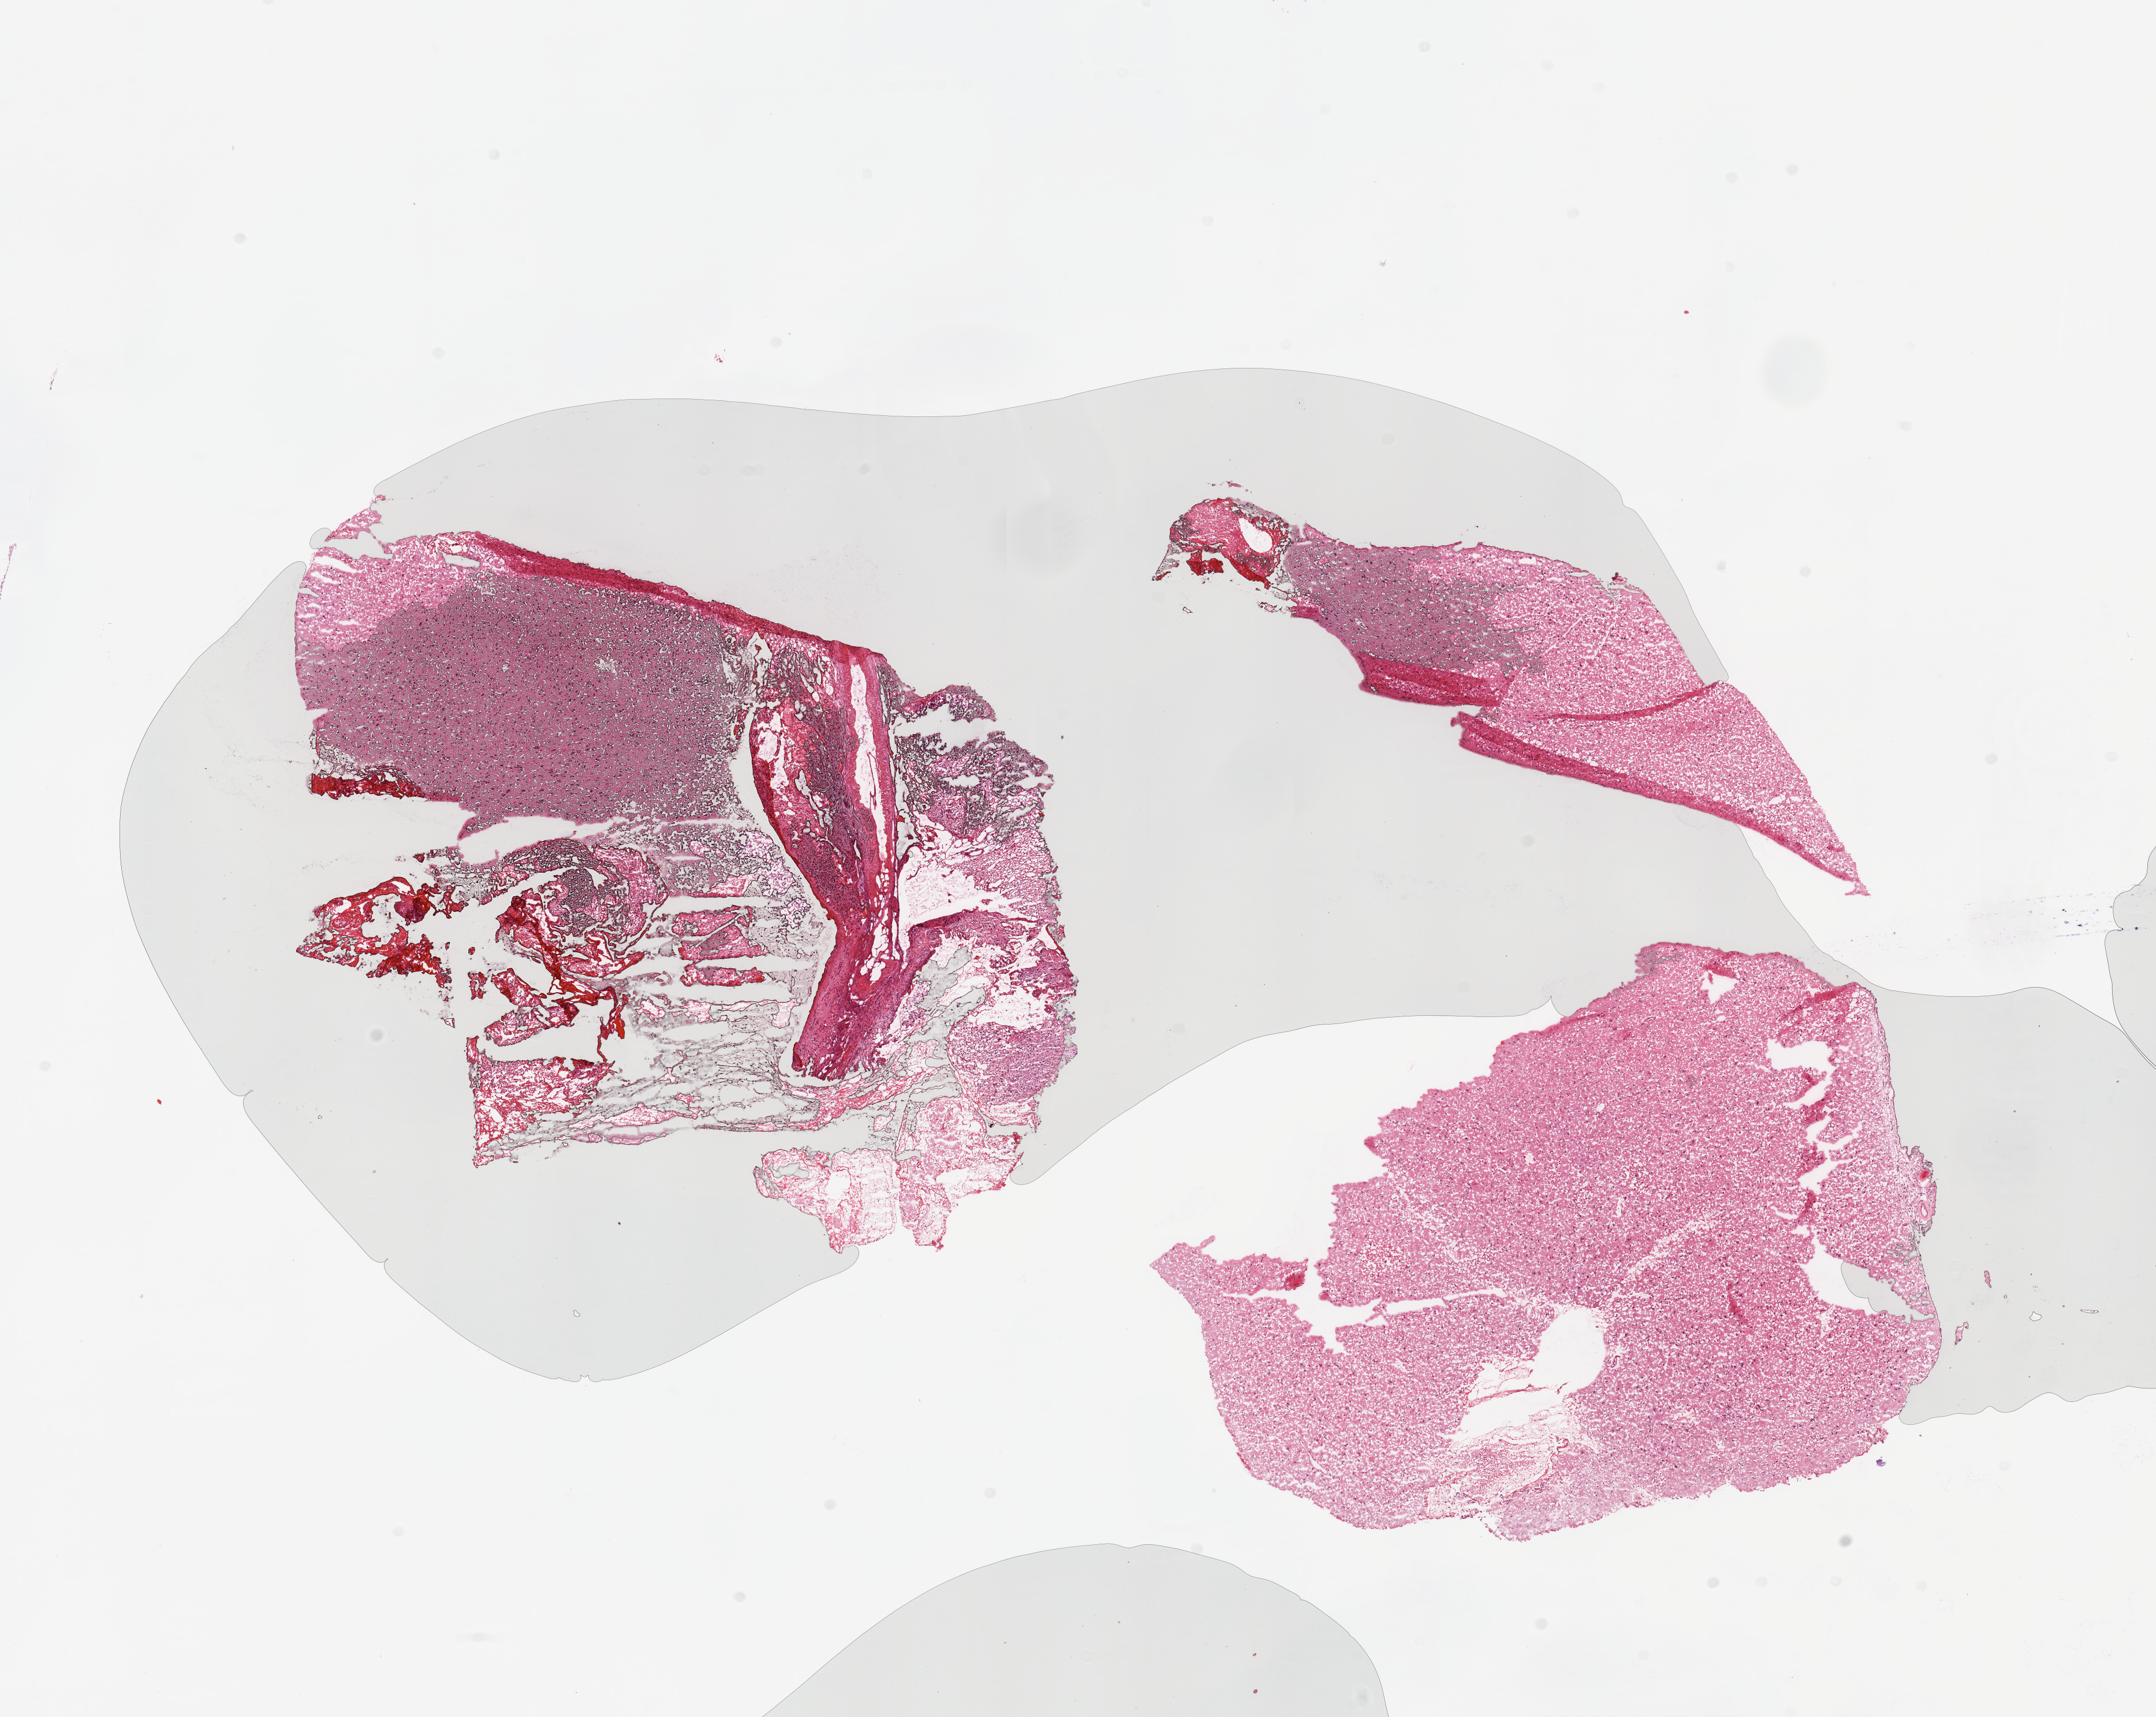
Whole-slide histology image, H&E-stained — a low-resolution overview of the entire scanned area, about 14.8 x 11.8 mm (from a 20x scan). Tumour tissue sample, brain. Male, 60 y/o.
Patient diagnosis (cohort enrolment): glioblastoma multiforme (brain). Primary tumour site (as recorded): parietal lobe.